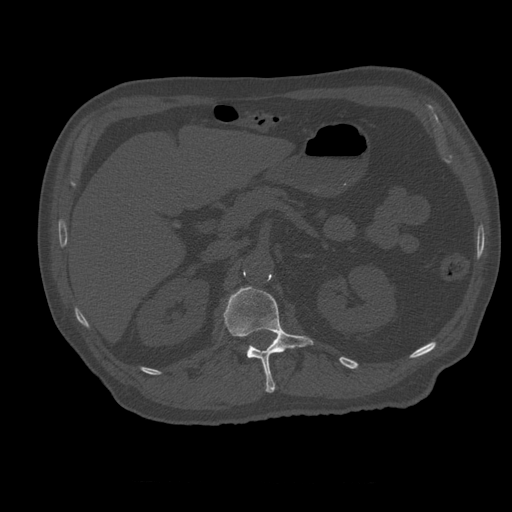
CT including the spine, one axial slice; slice 236 of 399 in the series (ordered by position); reconstruction kernel STANDARD; 120 kVp; bone window (W 1800 / L 400 HU); 1.25 mm slice thickness; 512 × 512 image matrix, field of view 407 × 407 mm. Patient age 73 years. From the clinical record (not read from this slice): primary cancer: prostate; vertebrae with lytic lesions (as recorded): L2.
Outlined on this slice (semi-automatic segmentation, software-assisted and operator-edited):
- L1 vertebra: box from (x=224, y=287) to (x=314, y=393) px